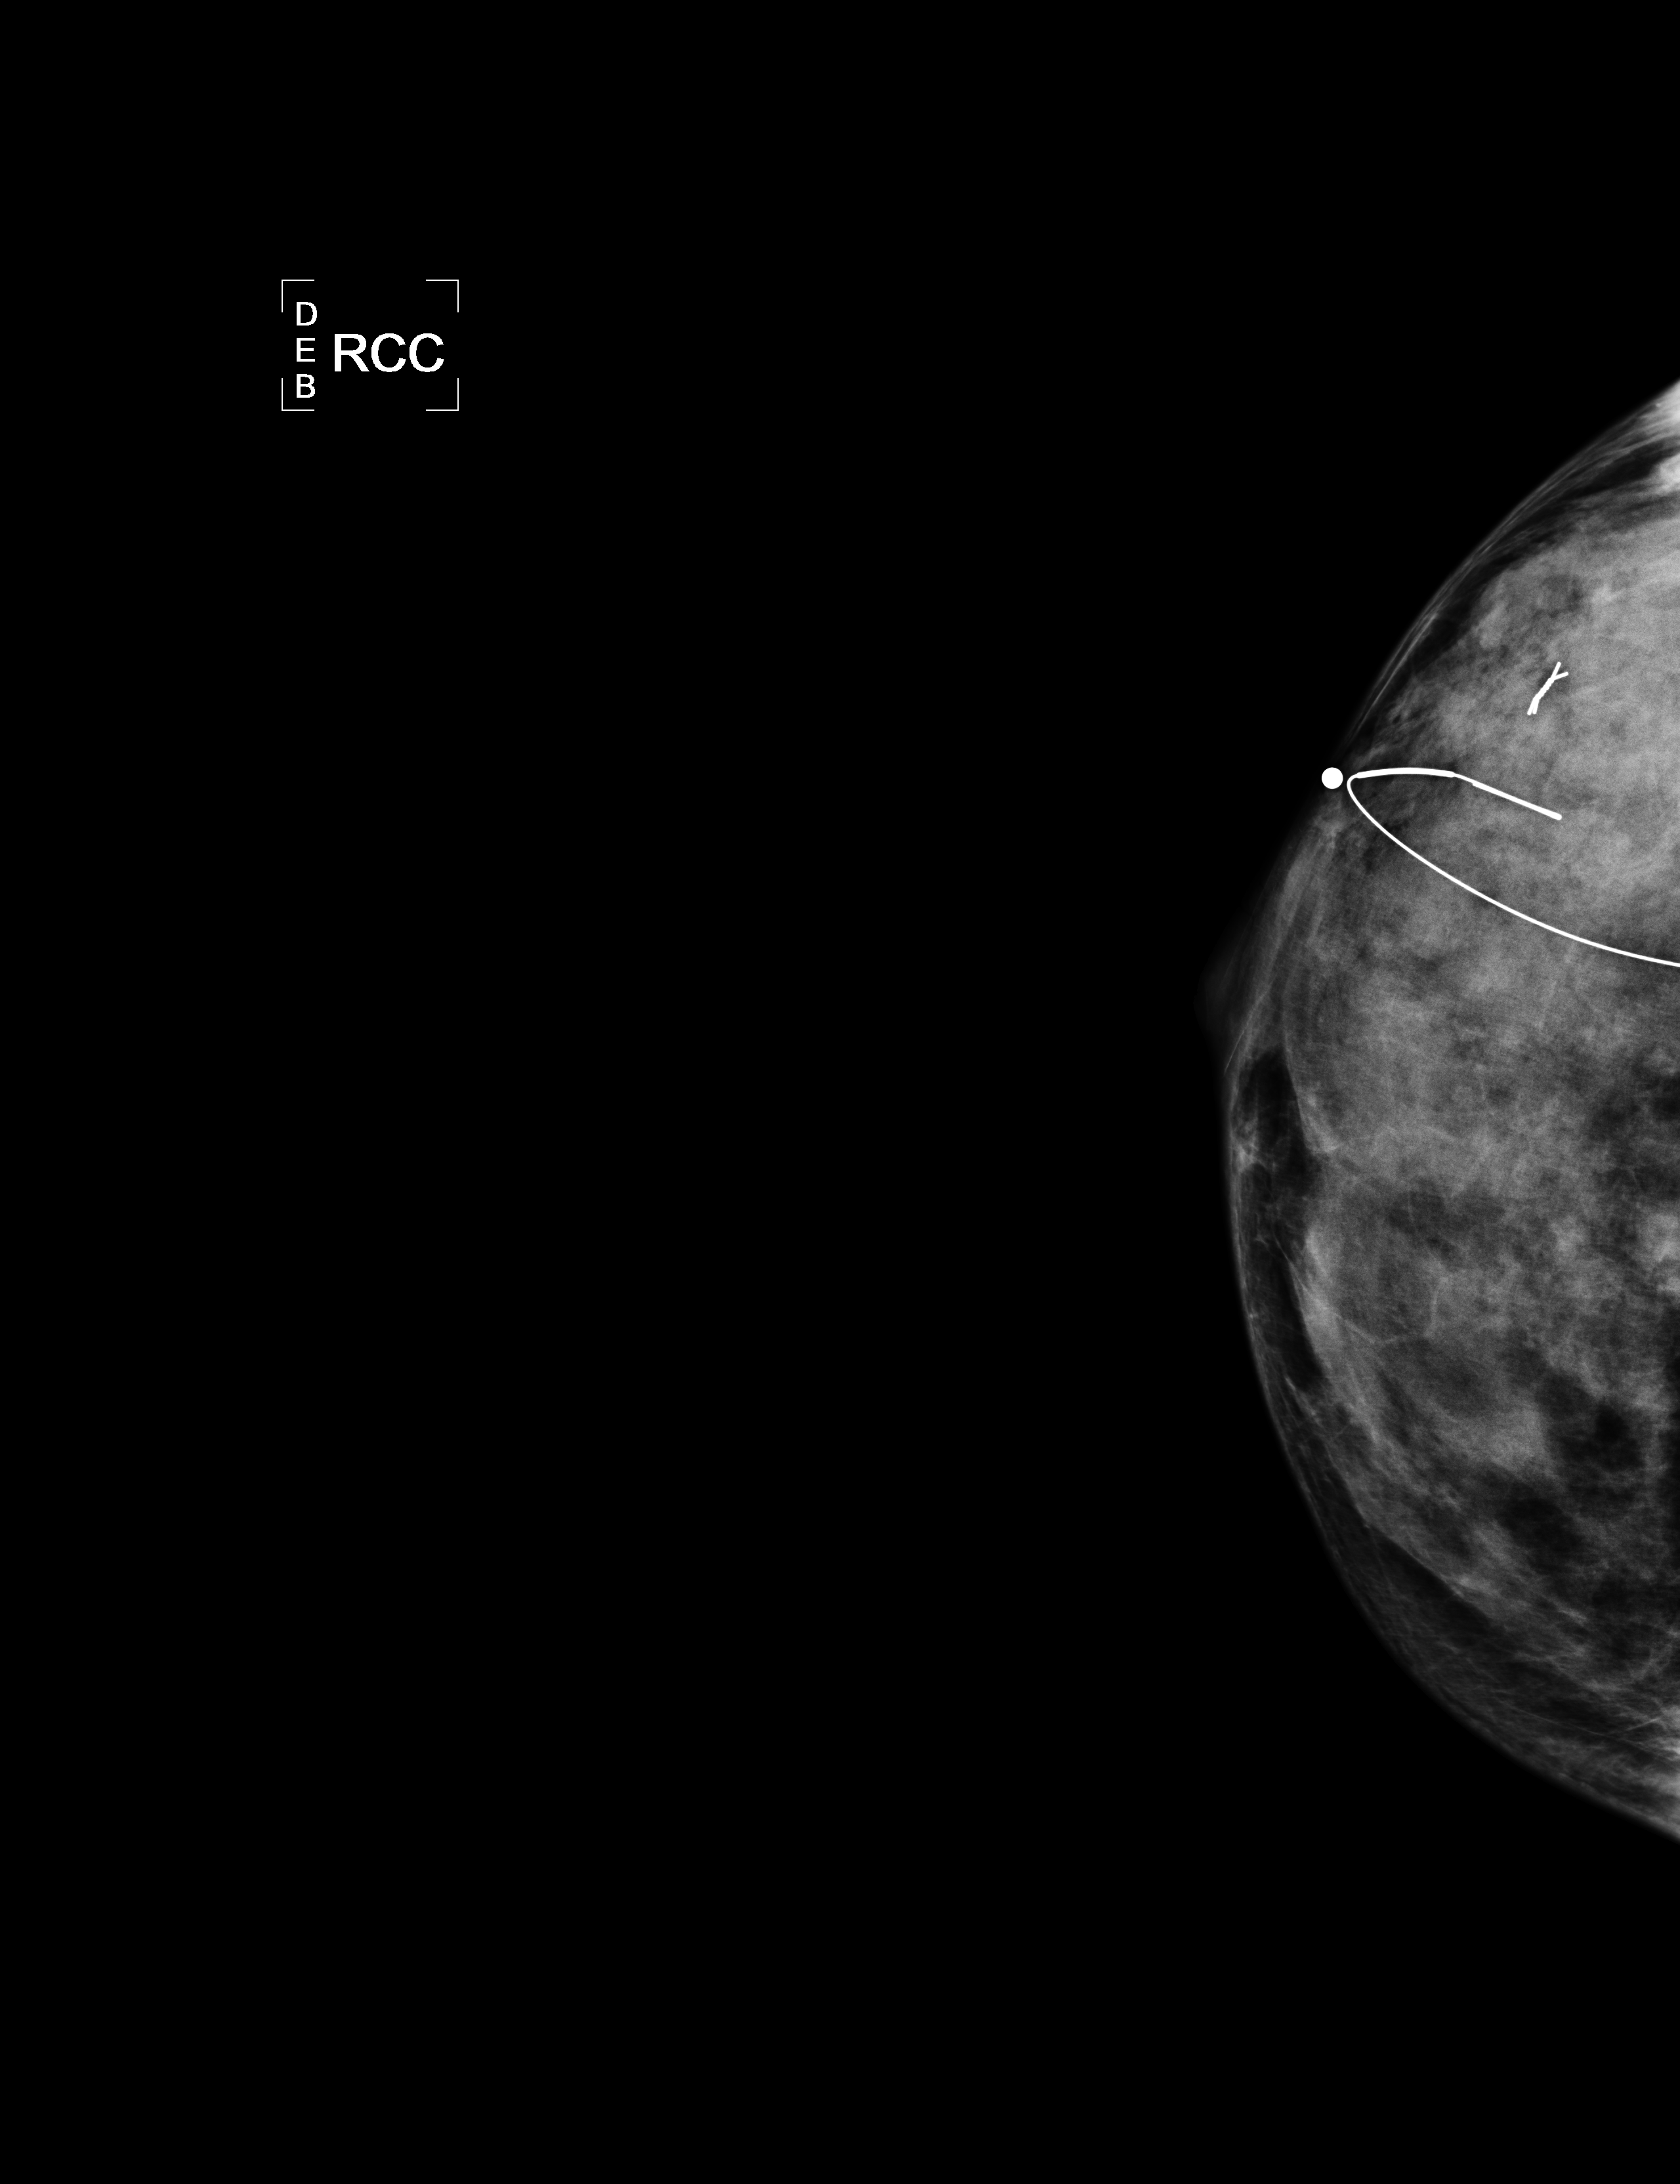
Mammogram, right breast, CC view.
Pathology recorded for this patient (not read from this image): pathology diagnosis: Invasive ductal carcinoma, modified Scarff-Bloom-Richardson grade II/III. No intraductal carcinoma component seen. (right breast); receptor status (as recorded): ER pos (strong), PR pos (strong), HER2 neg (weak); clinical background (as recorded): late 20's y.o. with bx-proven CA.